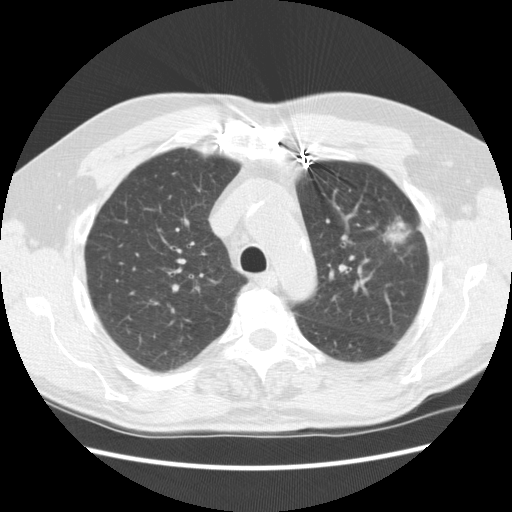
Low-dose screening chest CT, one axial slice. Slice 178 of 231 in the series (ordered by position). Lung window (W 1500 / L -600 HU). 2.5 mm slice thickness. 512 × 512 image matrix, field of view 362 × 362 mm.
Outlined on this slice (manually delineated by an expert):
- lesion 1 (tumor, upper lobe of left lung): bounding box [x1, y1, x2, y2] px = [383, 223, 408, 245]